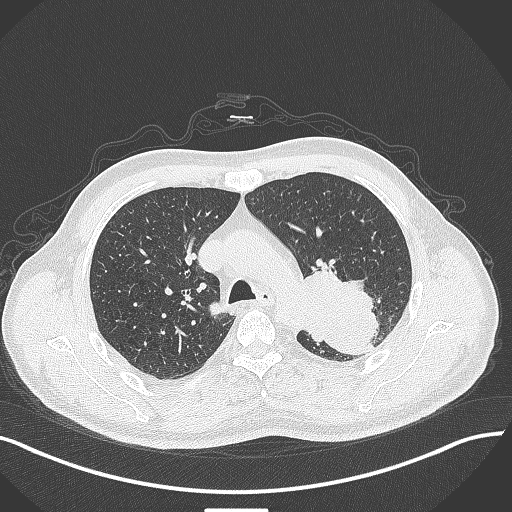
Chest CT, one axial slice; position 301 of 429 along the scan axis; lung window (W 1500 / L -600 HU); 1 mm slice thickness; 512 × 512 image matrix, field of view 400 × 400 mm. Male patient, age 55 years. From the clinical record (not read from this slice): clinical TNM (as recorded): T3 N0 M1c.
Outlined on this slice (bounding box drawn by a radiologist):
- lung tumour (recorded histology: adenocarcinoma): bounding box [x1, y1, x2, y2] px = [299, 265, 380, 361]